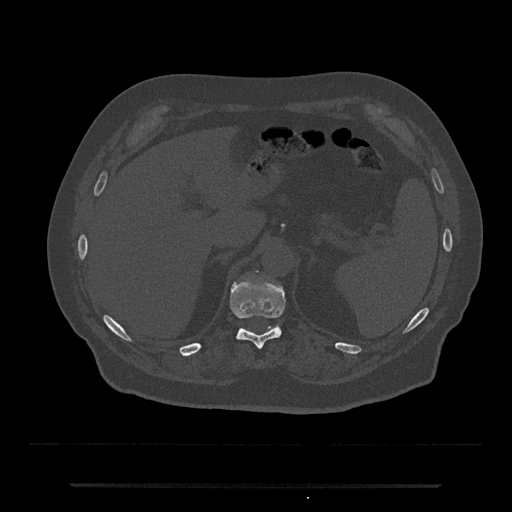
CT including the spine, one axial slice; slice 643 of 797 in the series (ordered by position); 120 kVp; bone window (W 1800 / L 400 HU); 0.5 mm slice thickness; 512 × 512 image matrix. Patient: male, 80 years. Case-level facts recorded for this patient, not image findings: primary cancer: prostate; vertebrae with lytic lesions (as recorded): L1, T11.
Structures marked on this image (semi-automatic segmentation, software-assisted and operator-edited):
- T11 vertebra: box from (x=230, y=283) to (x=285, y=349) px
- T12 vertebra: (x=242, y=270)–(x=279, y=329)